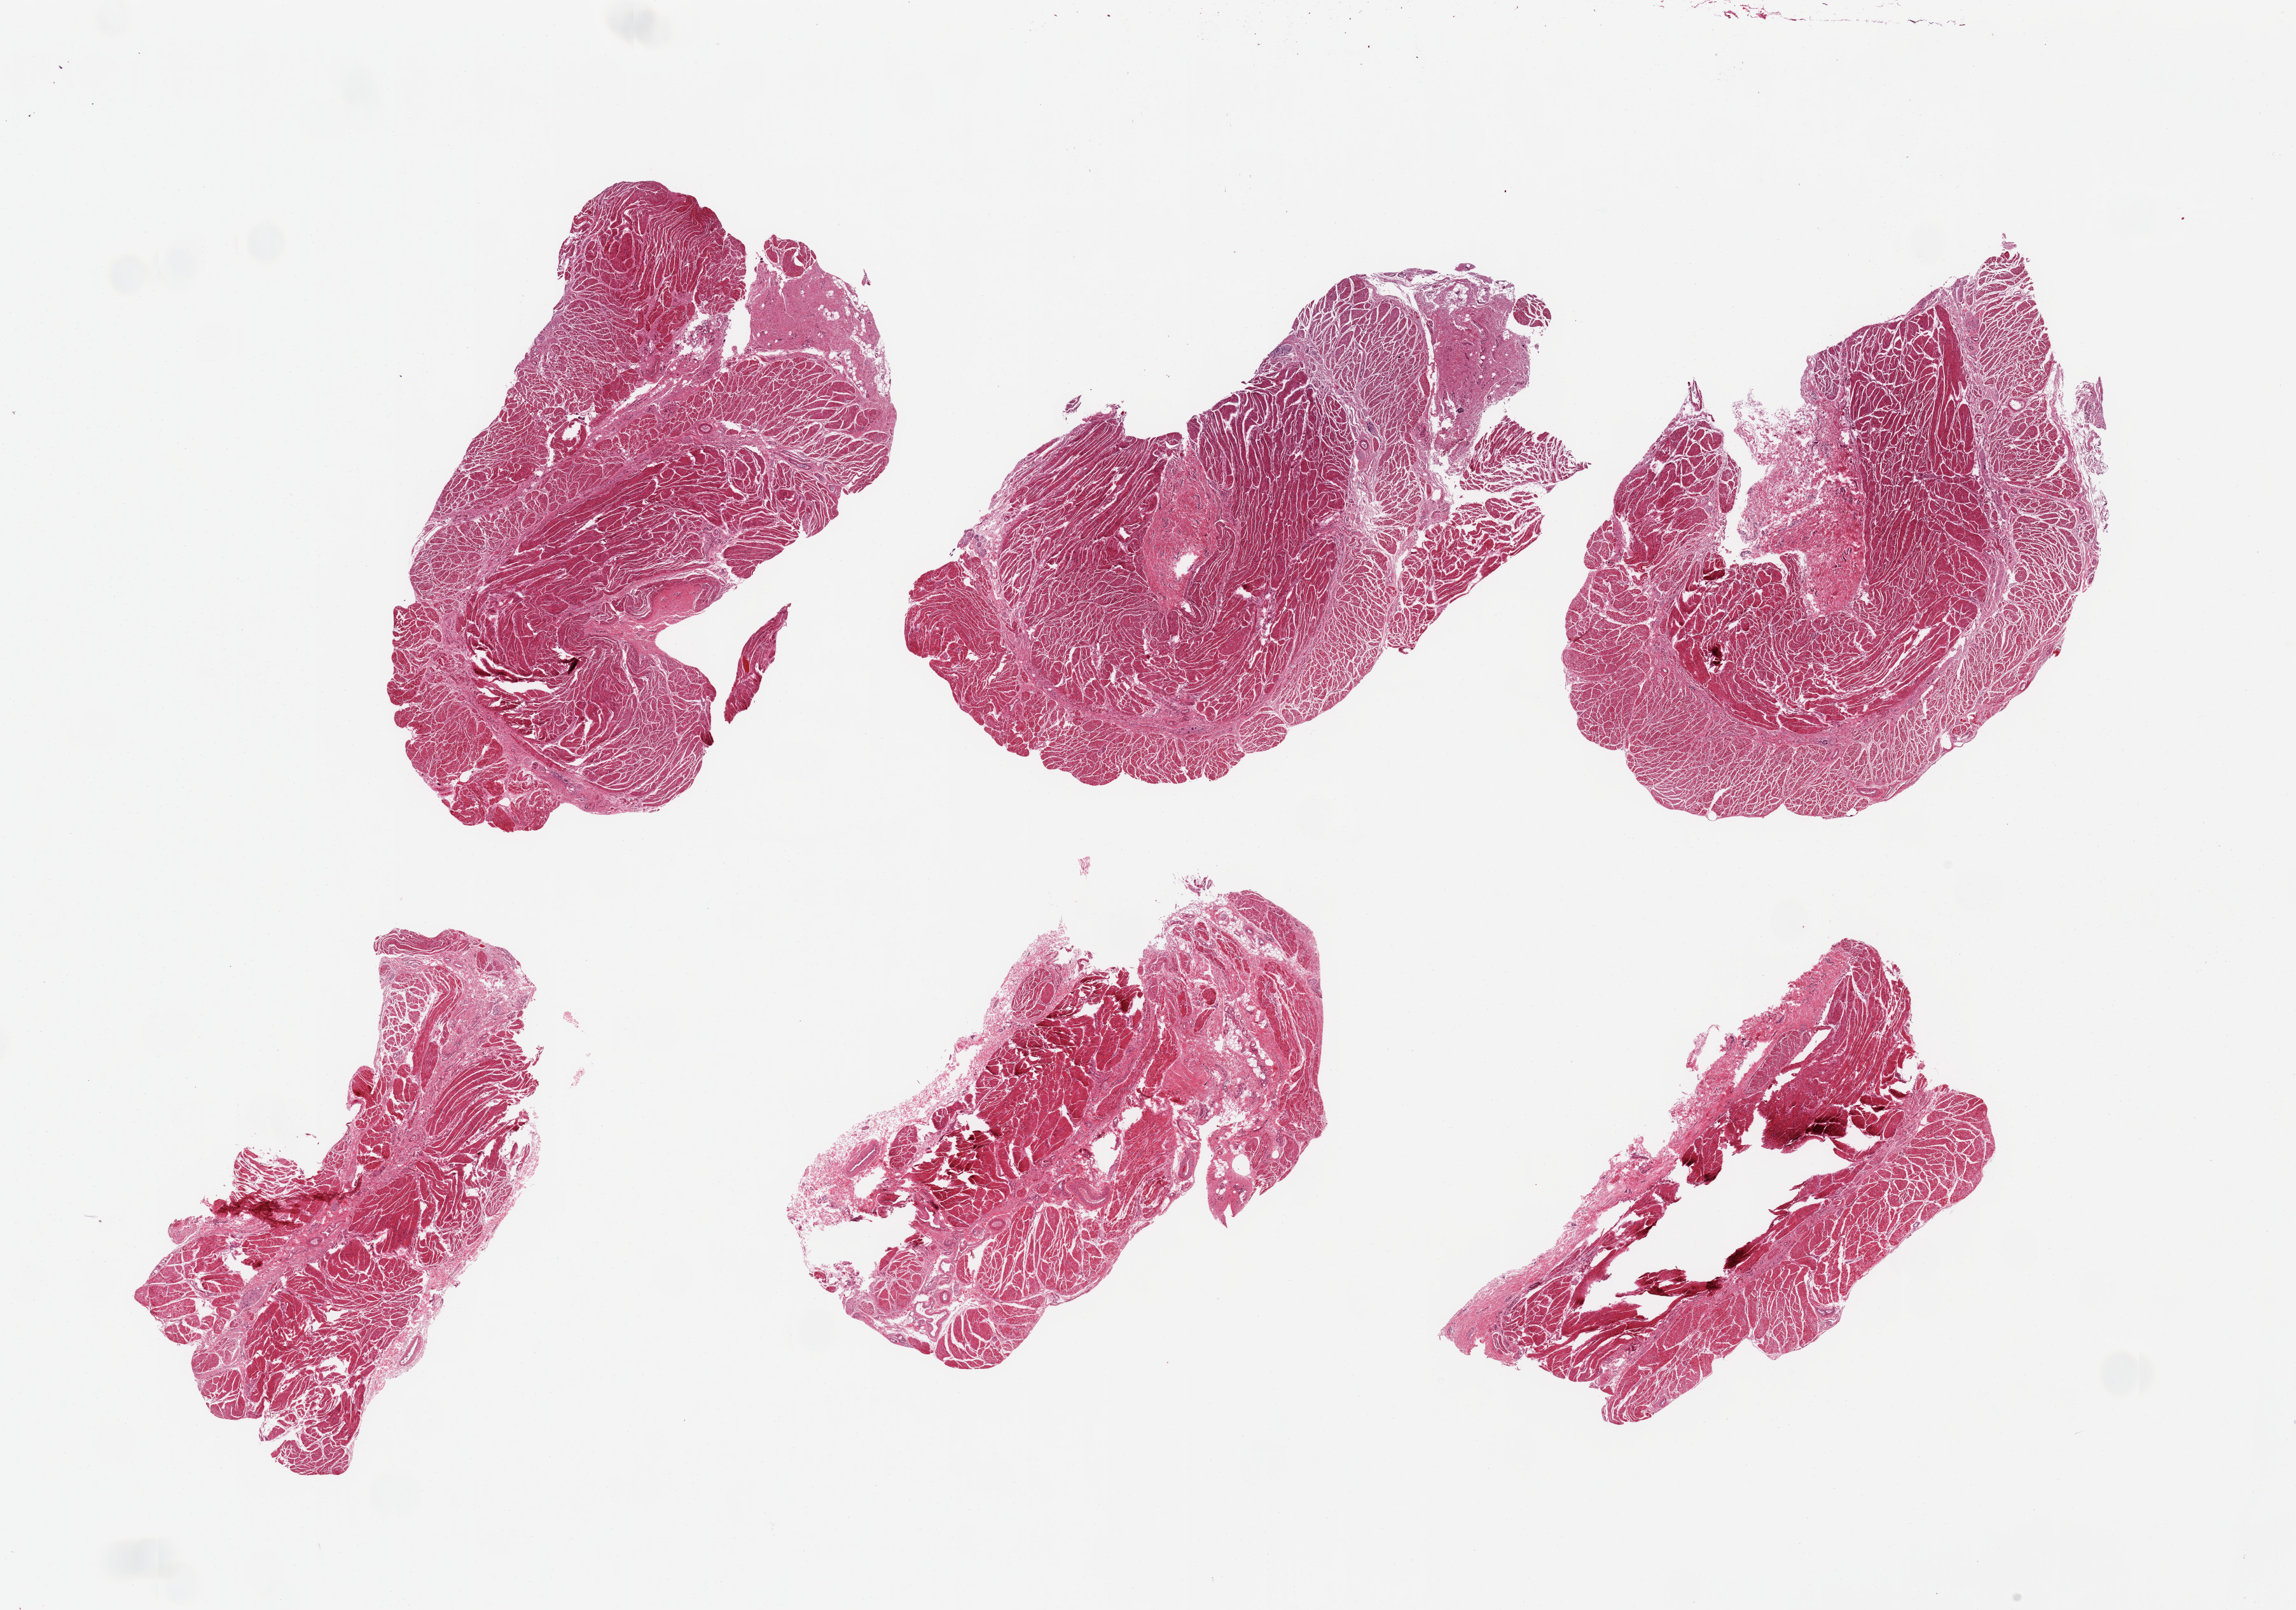
Whole-slide image, haematoxylin and eosin stain, shown as a low-resolution overview of the whole scanned area (about 28.5 x 20.0 mm, acquisition: 20x scan); PAXgene-fixed, paraffin-embedded tissue; section of esophageal muscle (target tissue); donor tissue sample.
Pathologist's review note for this sample: 6 pieces, conifrmed target muscularis.